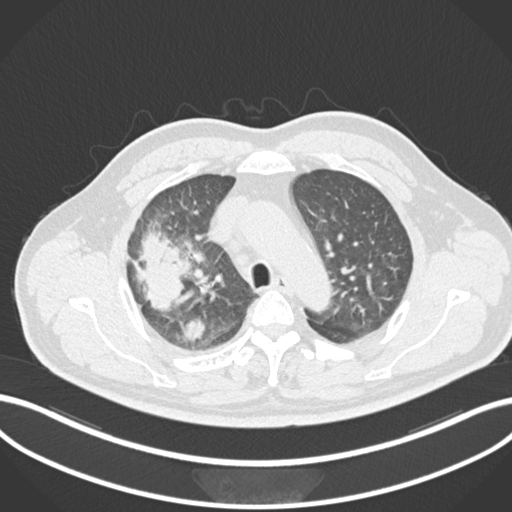
Chest CT, one axial slice. Position 672 of 852 along the scan axis. 120 kVp. Lung window (W 1500 / L -600 HU). 1 mm slice thickness. 512 × 512 image matrix, field of view 400 × 400 mm. Male patient, age 55 years. From the clinical record (not read from this slice): clinical TNM (as recorded): T3 N2 M1.
Outlined on this slice (rectangle marked by the reading radiologist):
- lung tumour (recorded histology: adenocarcinoma): bounding box (x1, y1, x2, y2) in pixels: (134, 225, 191, 314)